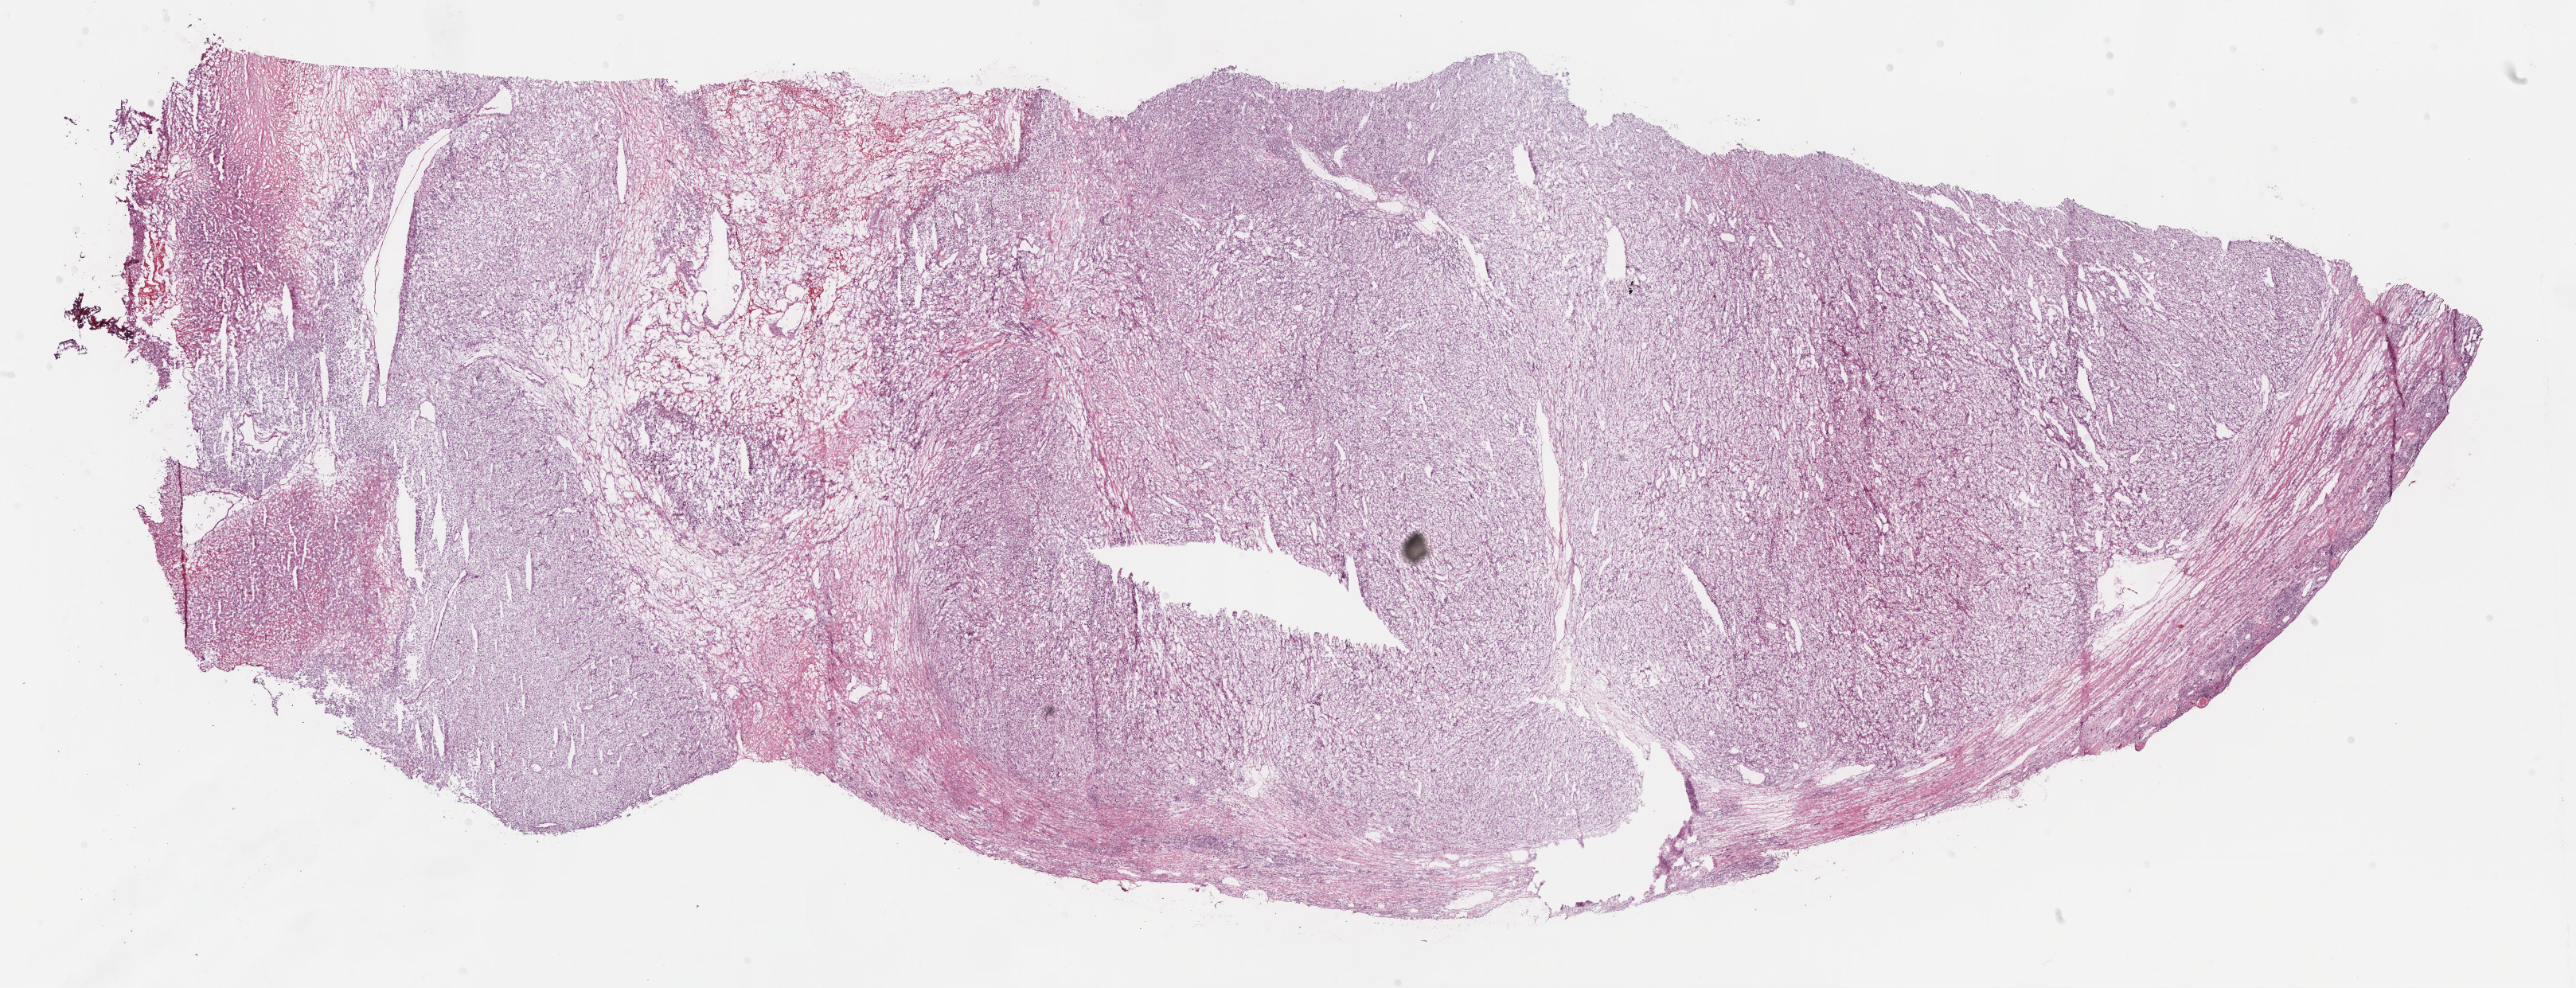
Whole-slide histology image, Hematoxylin and eosin (H&E) stained, a low-resolution overview of the entire scanned area, about 26.2 x 10.0 mm, frozen section from the bottom of the tissue portion, primary tumour sample from the kidney. Male patient; age at initial diagnosis 51 years. Histologic grade: G4 (undifferentiated). Slide review estimates, as recorded: tumour cells 70%, tumour nuclei 80%, normal cells 10%, stromal cells 10%, necrosis 10%.
• pathologic diagnosis: Clear cell adenocarcinoma, NOS
• laterality: left
• AJCC pathologic stage: IV